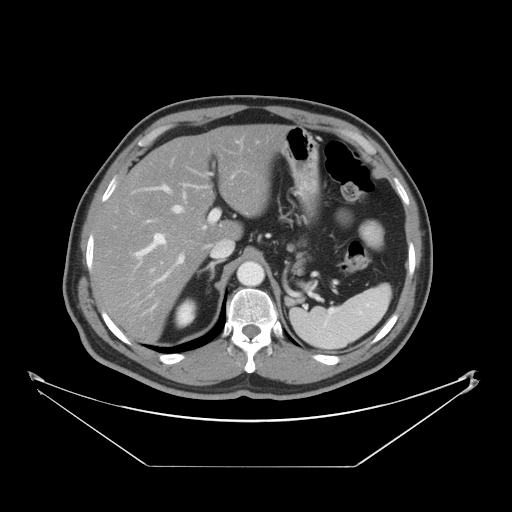
Contrast-enhanced abdominal CT, one axial slice. Slice 30 of 46 in the series (ordered by position). Intravenous contrast given. Soft-tissue window (W 400 / L 40 HU). 5 mm slice thickness. 512 × 512 image matrix, field of view 465 × 465 mm. Male patient, age 57 years. Case-level facts recorded for this patient, not image findings: diagnosis: colorectal cancer liver metastases, imaged before liver resection; multiple liver metastases: no.
Structures marked on this image (manually delineated by an expert):
- hepatic veins: bounding box <145,184,184,223> (left, top, right, bottom; pixels)
- liver: <94,127,283,340>
- planned liver remnant (the part of the liver to remain after resection): <94,127,283,340>
- portal vein (with intrahepatic branches): <131,209,220,300>